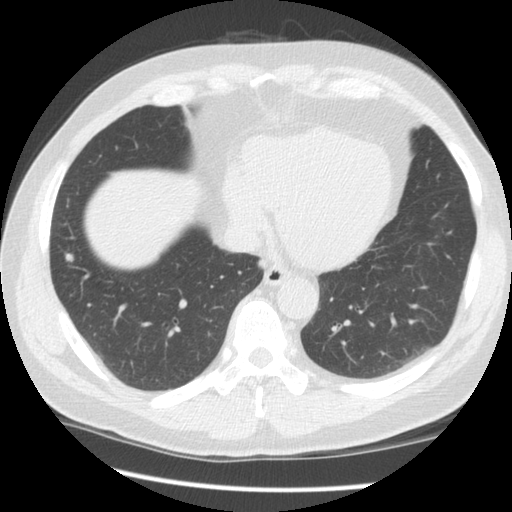
Axial slice from a low-dose chest CT screening exam, second annual screen, lung window (W 1500 / L -600 HU), slice 52 of 135 in the series. Male, age 61 years at enrolment. Current smoker at enrolment.
Expert reader's lesion annotation, box from (x=49, y=242) to (x=87, y=278) px. Reader record for this screening exam (exam-level; its link to the box is not recorded): non-calcified nodule or mass ≥4 mm, right lower lobe, 5 × 4 mm, smooth margins, soft tissue attenuation, pre-existing on the prior screen: no. Official screen result: positive, other. Later outcome: lung cancer diagnosed 311 days after this screen — small cell carcinoma, NOS, right hilum, undifferentiated (G4), stage IV (AJCC 6th edition), 140 mm at pathology.